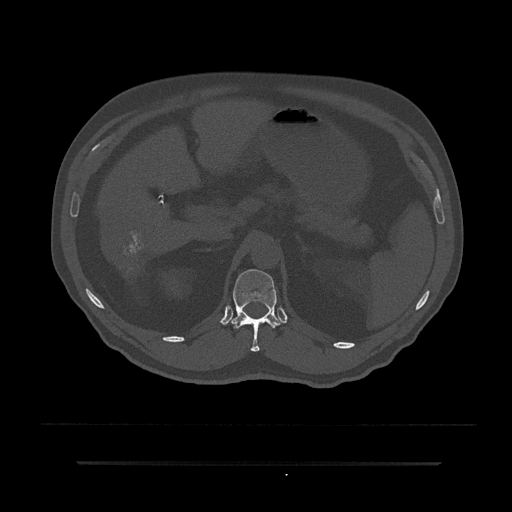
CT including the spine, one axial slice. Reconstruction kernel Br40s/3. 120 kVp. Bone window (W 1800 / L 400 HU). 512 × 512 image matrix, field of view 464 × 464 mm. Patient: male, 59 years. Case-level facts recorded for this patient, not image findings: primary cancer: bile ducts; vertebrae with lytic lesions (as recorded): T10.
Outlined on this slice (semi-automatic segmentation, software-assisted and operator-edited):
- T12 vertebra: bounding box <231,269,281,352> (left, top, right, bottom; pixels)